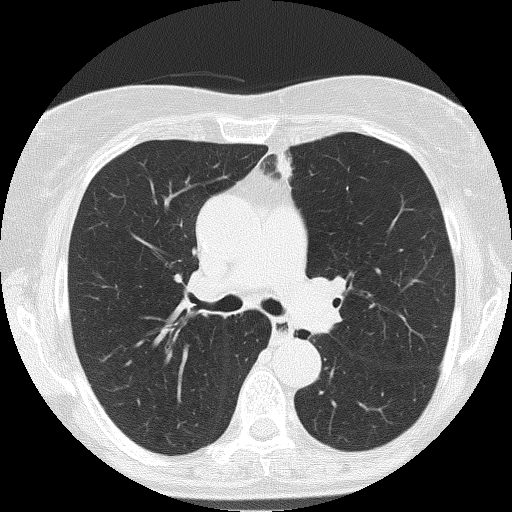
Low-dose screening chest CT, one axial slice. Position 109 of 166 along the scan axis. 120 kVp. Lung window (W 1500 / L -600 HU). 2 mm slice thickness. 512 × 512 image matrix, field of view 303 × 303 mm.
Annotated regions visible in this slice (outlined manually by an expert reader):
- lesion 2 (nodule, upper lobe of left lung): bounding box (x1, y1, x2, y2) in pixels: (276, 153, 290, 180)